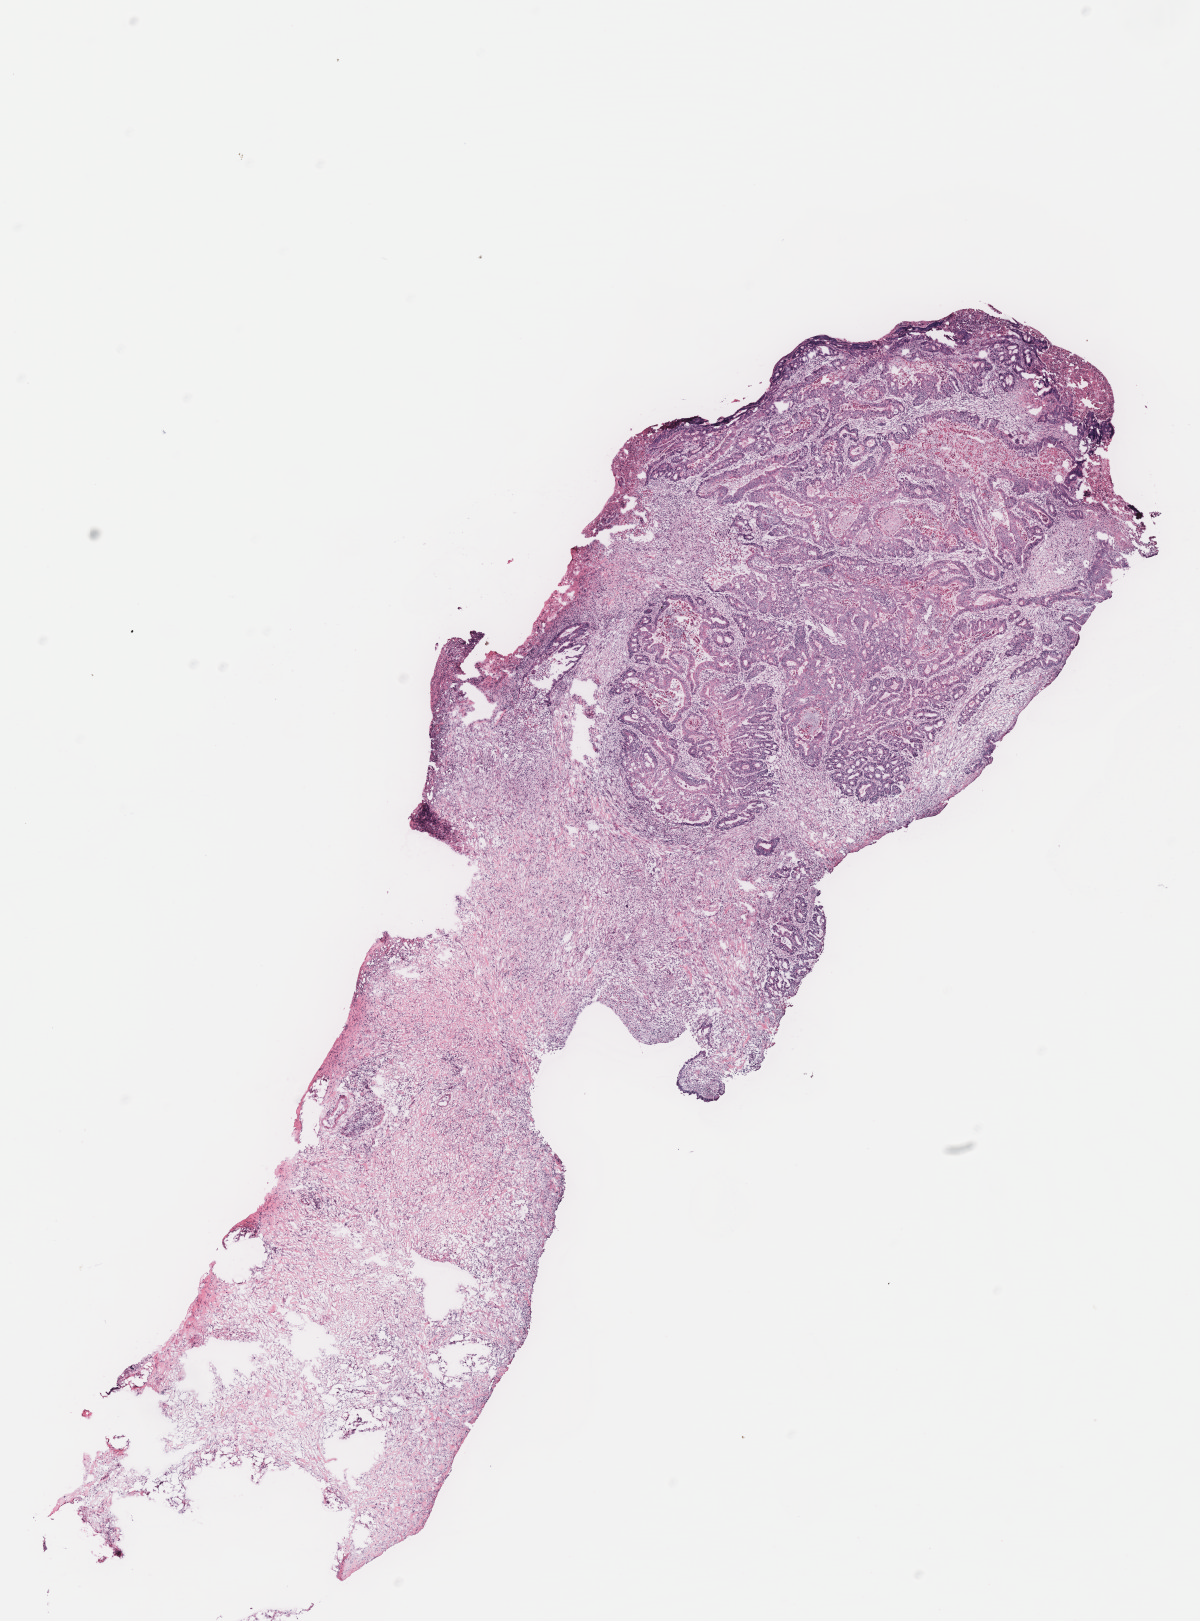
Hematoxylin and eosin (H&E) stained whole-slide image, a low-resolution overview of the entire scanned area, about 9.6 x 13.0 mm (acquisition: 40x scan); colon, tissue type not recorded.
* patient diagnosis (cohort enrolment): colon cancer (colon)